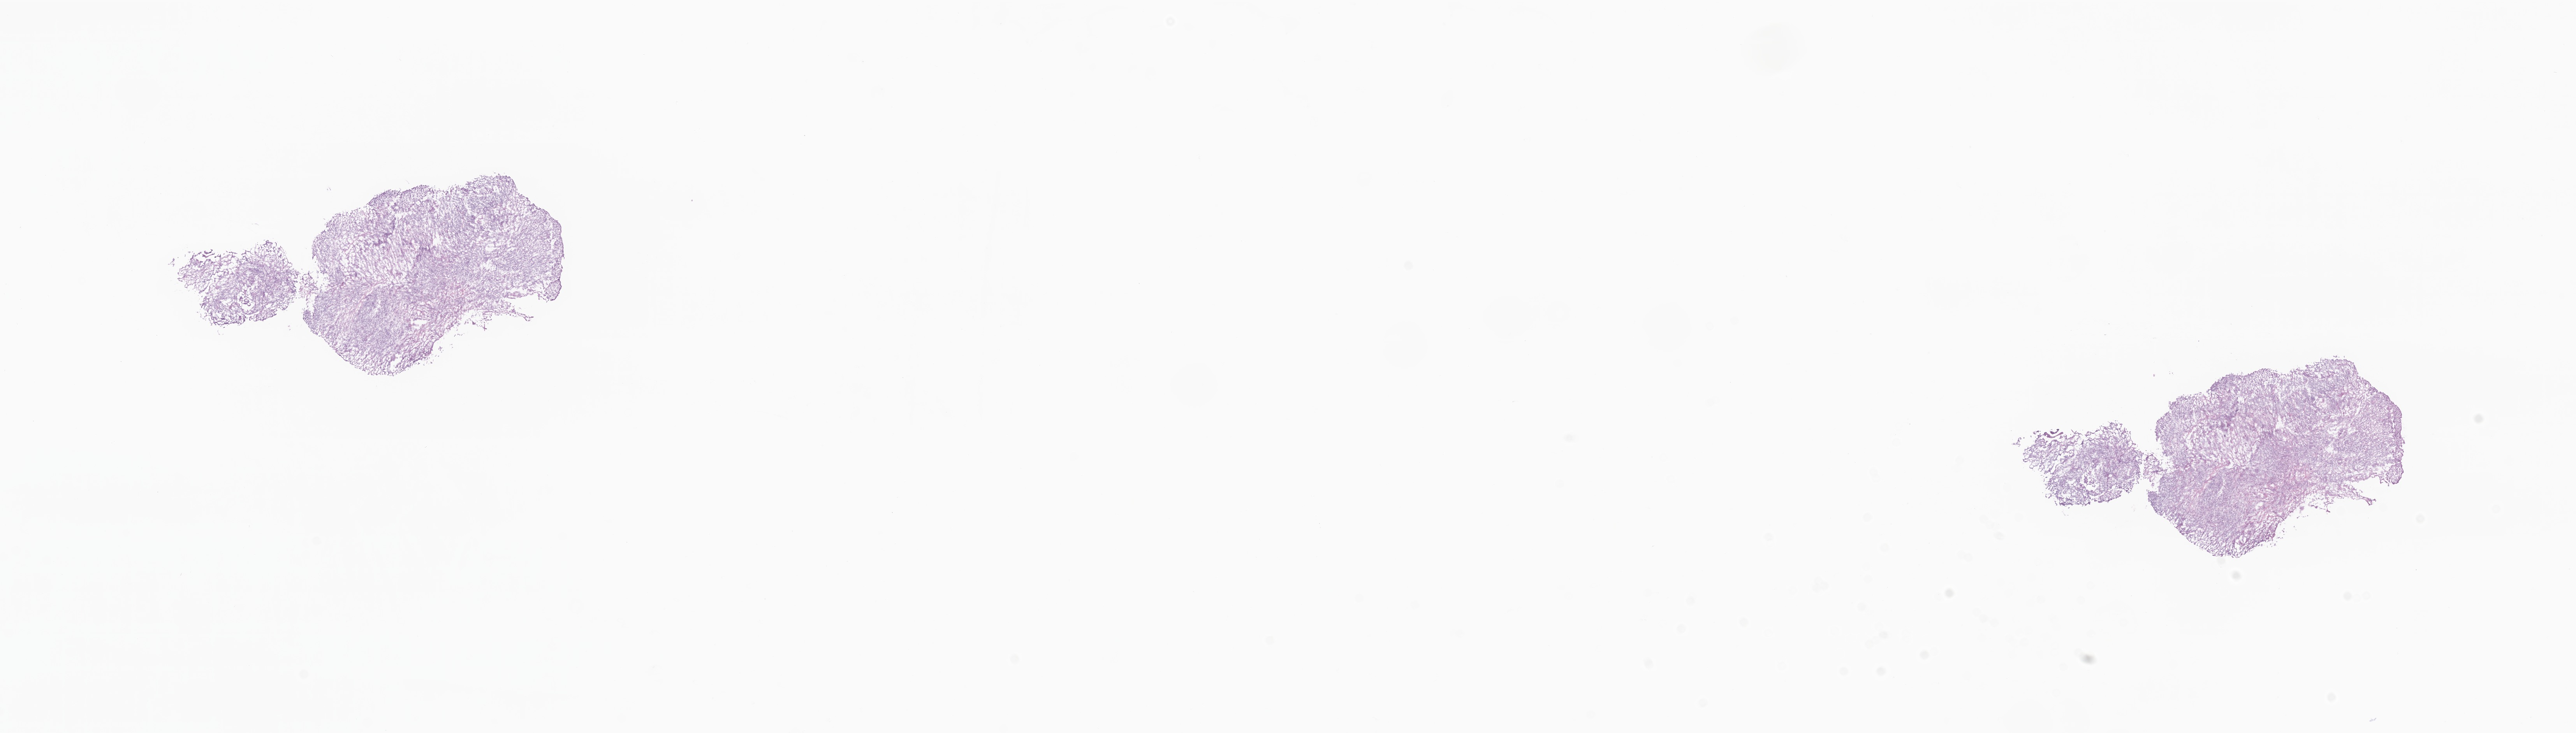
Digitized hematoxylin and eosin (H&E)-stained section, a low-resolution overview of the entire scanned area, about 27.9 x 7.9 mm, frozen section (tissue freezing medium), primary tumor, anatomic site: lower lobe of left lung. Male, age 82 years at initial diagnosis. Pathologist review of this section (percent, as recorded): tumor cells 40%, tumor nuclei 50%, stromal cells 60%, necrosis 0%, normal cells 0%. Infiltration values recorded for this section: lymphocyte infiltration 100%, monocyte infiltration 0%, neutrophil infiltration 0%.
Histologic diagnosis: Squamous cell carcinoma, NOS. Section: bottom of the tissue portion.